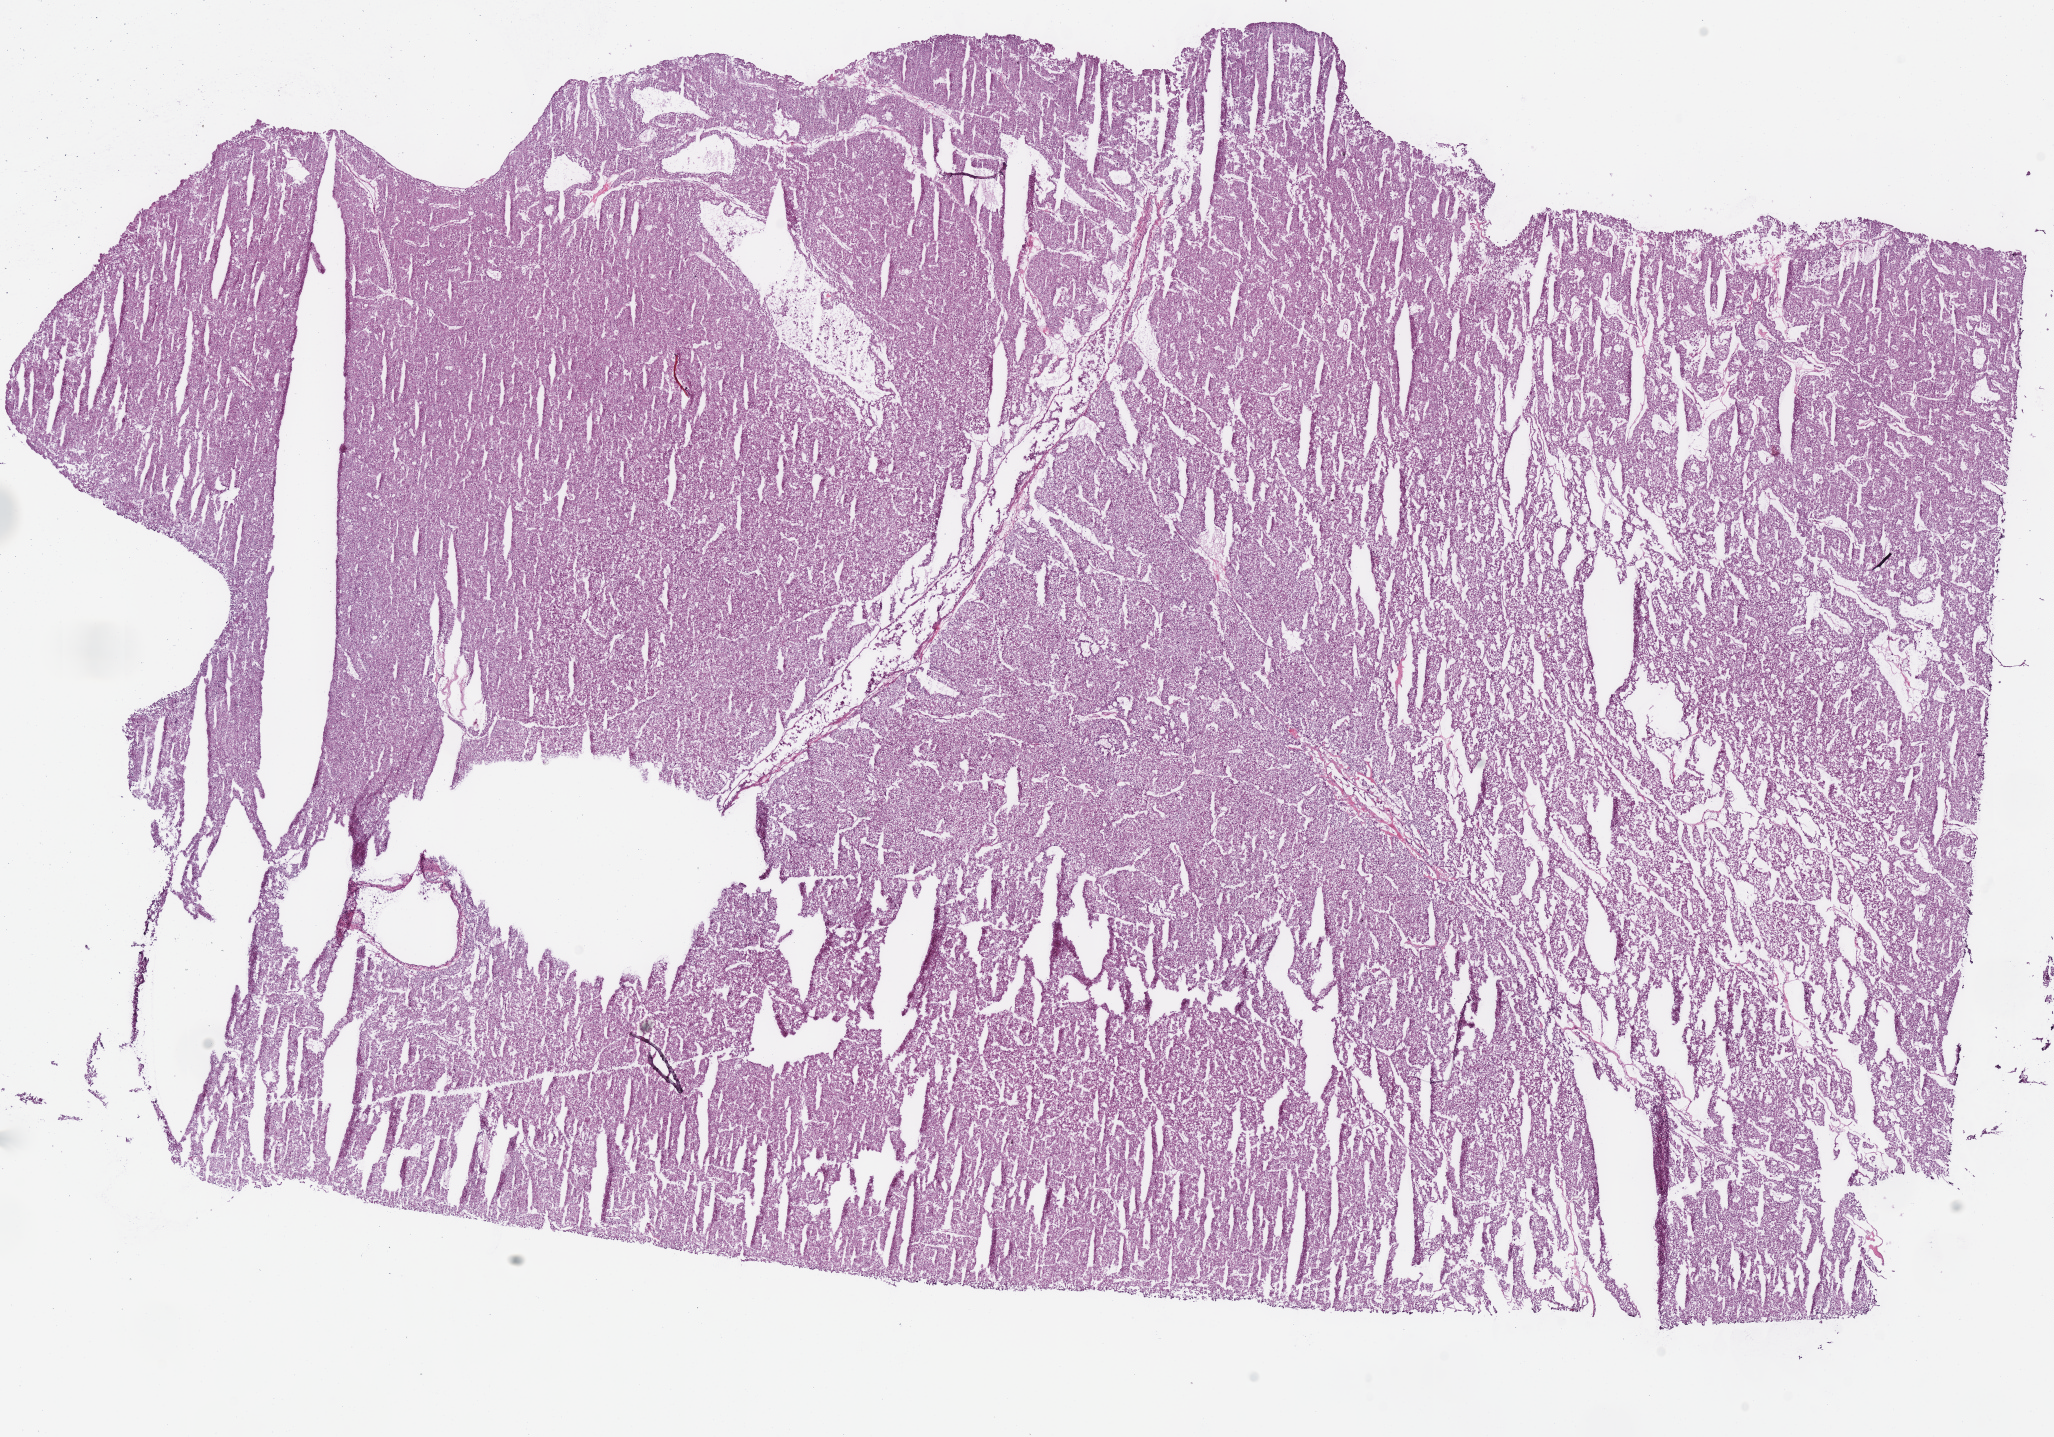
Hematoxylin and eosin (H&E) stained whole-slide image, low-resolution overview of the scanned area, about 16.2 x 11.3 mm (from a 40x scan); frozen section from the bottom of the tissue portion; sample: primary tumour, kidney. Female, age 44 years at initial diagnosis. Pathologist review of this section (percent, as recorded): tumour cells 100%, tumour nuclei 95%, normal cells 0%, stromal cells 0%, necrosis 0%. Inflammatory infiltration, as recorded: lymphocyte infiltration 0%, monocyte infiltration 0%, neutrophil infiltration 0%.
* lymph nodes positive (case pathology): 0 of 8 examined
* AJCC pathologic stage: II (6th edition)
* histologic diagnosis: Renal cell carcinoma, chromophobe type